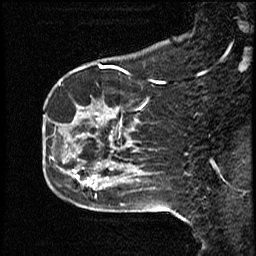
Breast MRI (dynamic contrast-enhanced), one sagittal slice. Slice 15 of 50 in the series (ordered by position). Dynamic contrast-enhanced study with each time point stored as its own series, time point 2 of 4 at this slice position (early post-contrast, ordered by acquisition time). 1.5 T. TE 4.2 ms, TR 18.5 ms. 3 mm slice thickness. 256 × 256 image matrix, field of view 200 × 200 mm. Female patient, age 44 years. From the clinical record (not read from this slice): setting: breast cancer imaged before/during neoadjuvant chemotherapy; receptor status: HR-positive, HER2-negative.
Outlined on this slice (semi-automatically segmented with operator editing):
- analysis volume of interest (the breast-tissue region the enhancement analysis was run in; not a lesion): bounding box [x1, y1, x2, y2] px = [59, 80, 114, 206]
- tumour enhancement mask (voxels above the 100 % enhancement threshold inside the analysis volume of interest): [75, 113, 98, 189]